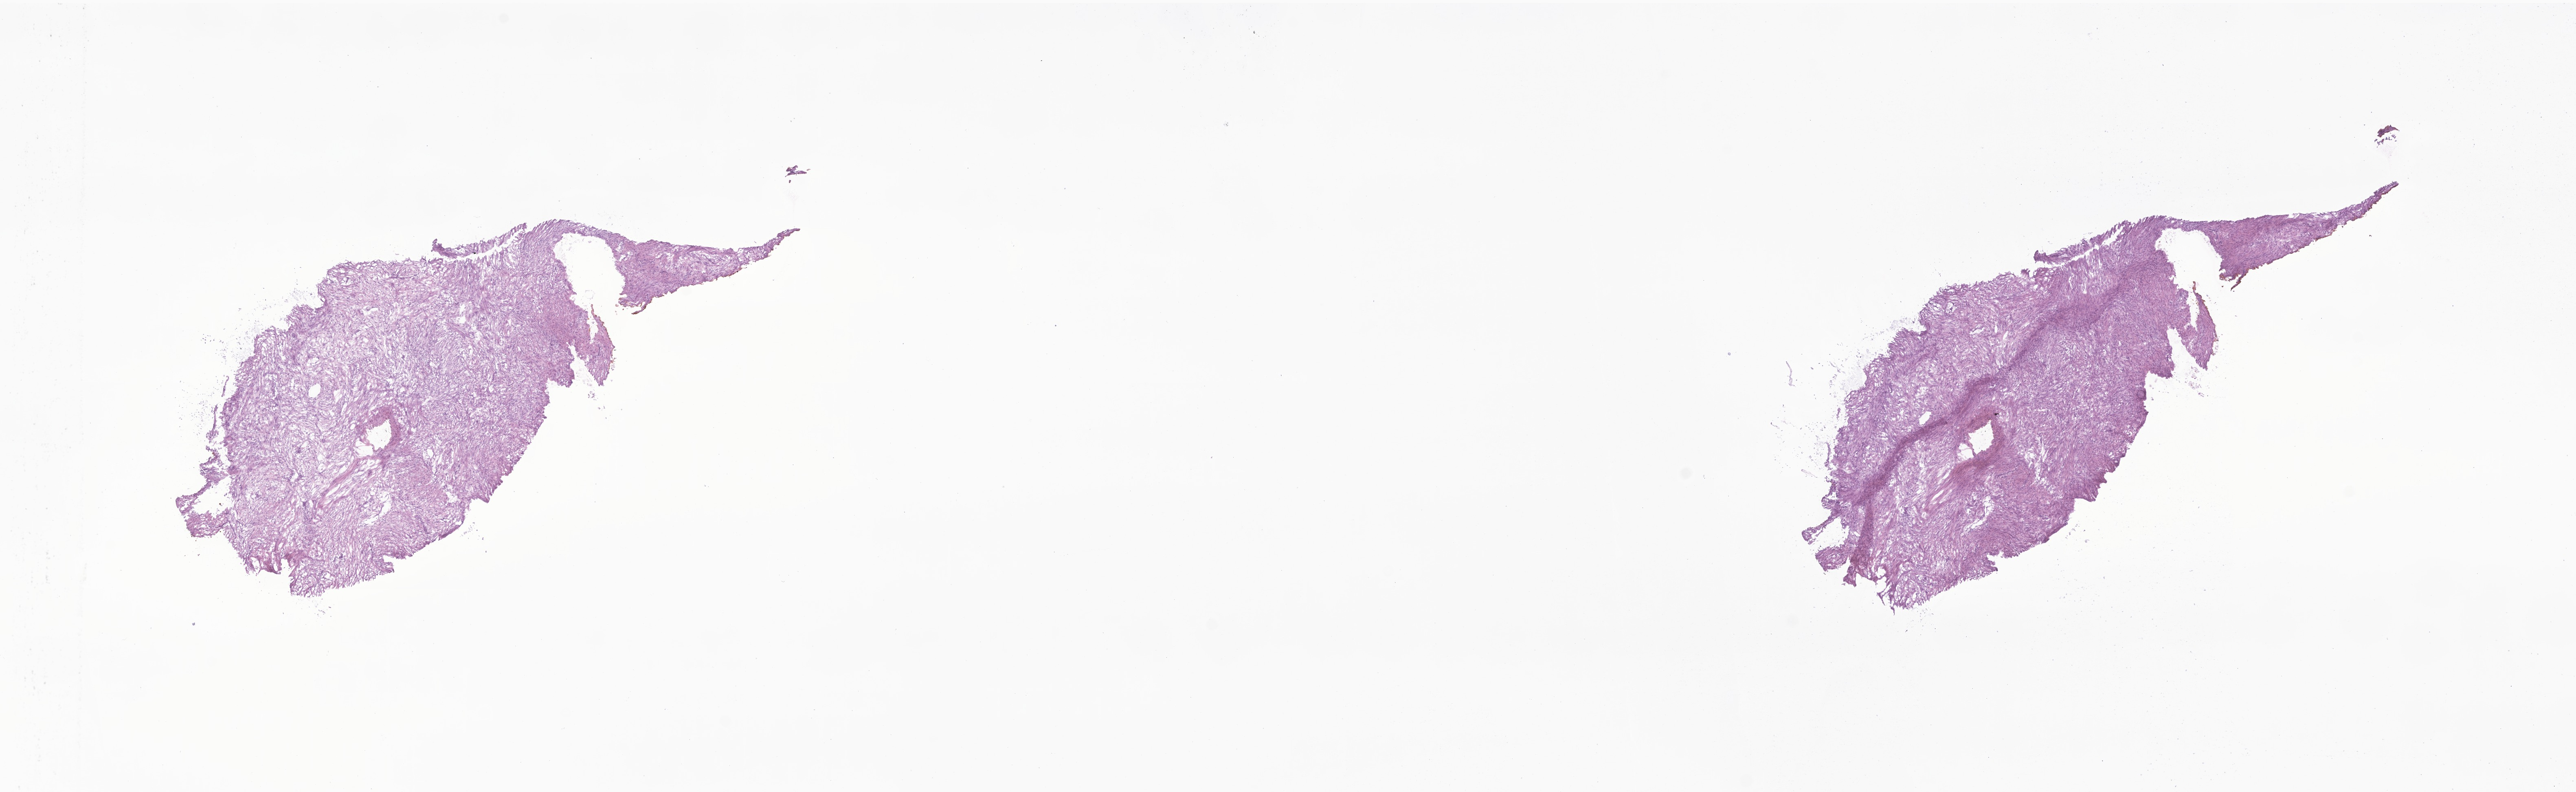
Whole-slide image, hematoxylin and eosin (H&E) stain of tumor tissue from the abdomen — whole scanned area (about 26.7 x 8.2 mm) shown as a low-resolution overview, cryosection (OCT / tissue freezing medium). Patient: female, age 212 months.
Diagnosis (ICD-O-3 morphology term): Abdominal fibromatosis.